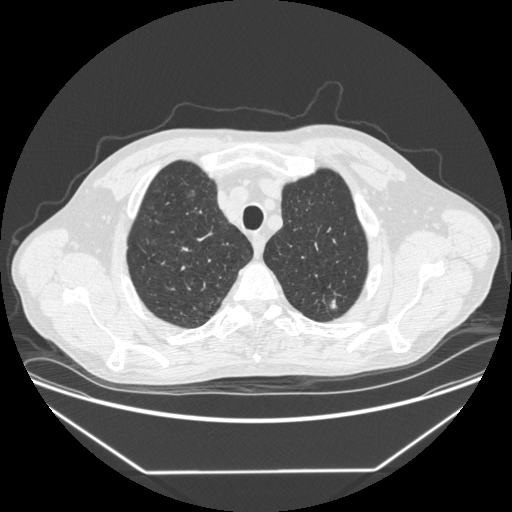
Low-dose screening chest CT, one axial slice; slice 332 of 383 in the series (ordered by position); reconstruction kernel STANDARD; 120 kVp; lung window (W 1500 / L -600 HU); 512 × 512 image matrix, field of view 418 × 418 mm.
Structures marked on this image (manually delineated by an expert):
- lesion 1 (tumor, upper lobe of left lung): bounding box (x1, y1, x2, y2) in pixels: (330, 299, 337, 309)